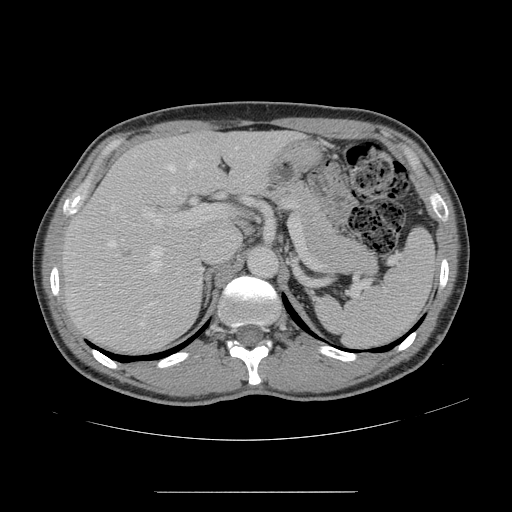
Contrast-enhanced abdominal CT, one axial slice. Position 97 of 178 along the scan axis. Intravenous contrast given. Soft-tissue window (W 400 / L 40 HU). 2.5 mm slice thickness. 512 × 512 image matrix, field of view 401 × 401 mm. Male patient, age 53 years. From the clinical record (not read from this slice): diagnosis: colorectal cancer liver metastases, imaged before liver resection; multiple liver metastases: yes; largest metastasis: 2.4 cm.
Structures marked on this image (manually delineated by an expert):
- hepatic veins: box from (x=108, y=146) to (x=238, y=326) px
- liver: (x=64, y=132)–(x=295, y=350)
- planned liver remnant (the part of the liver to remain after resection): (x=147, y=133)–(x=296, y=193)
- portal vein (with intrahepatic branches): (x=144, y=205)–(x=223, y=306)